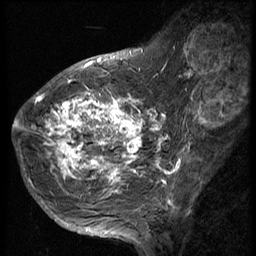
Breast MRI (dynamic contrast-enhanced), one sagittal slice. Slice 20 of 56 in the series (ordered by position). 3 images stored at this slice position (order not interpretable as contrast timing). 1.5 T. TE 4.2 ms, TR 9 ms. 256 × 256 image matrix, field of view 180 × 180 mm. Patient: female, 49 years. Case-level facts recorded for this patient, not image findings: setting: breast cancer imaged before/during neoadjuvant chemotherapy; receptor status: HER2-positive.
Outlined on this slice (semi-automatic segmentation, software-assisted and operator-edited):
- analysis volume of interest (the breast-tissue region the enhancement analysis was run in; not a lesion): box from (x=37, y=85) to (x=145, y=207) px
- tumour enhancement mask (voxels above the 140 % enhancement threshold inside the analysis volume of interest): (x=37, y=97)–(x=143, y=204)